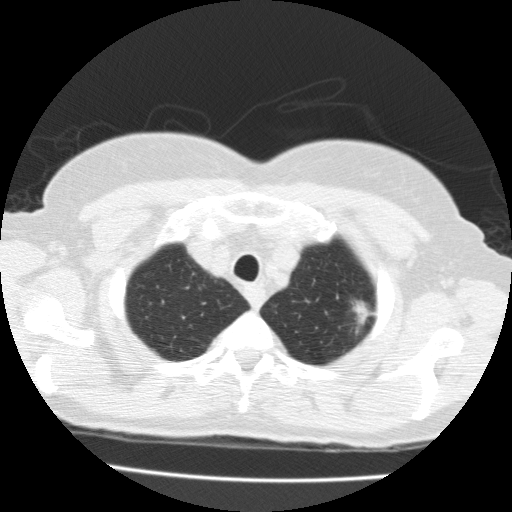
Low-dose screening chest CT, one axial slice; slice 161 of 183 in the series (ordered by position); reconstruction kernel FC10; lung window (W 1500 / L -600 HU); 2 mm slice thickness; 512 × 512 image matrix, field of view 320 × 320 mm.
Structures marked on this image (manually delineated by an expert):
- lesion 1 (tumor, upper lobe of left lung): bounding box (x1, y1, x2, y2) in pixels: (353, 301, 371, 324)